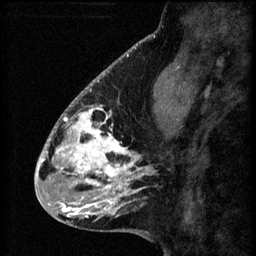
Breast MRI (dynamic contrast-enhanced), one sagittal slice. Position 20 of 60 along the scan axis. 3 images stored at this slice position (order not interpretable as contrast timing). 1.5 T. TE 4.2 ms, TR 8.2 ms. 2.2 mm slice thickness. 256 × 256 image matrix. Female patient, age 41 years.
Outlined on this slice (semi-automatically segmented with operator editing):
- analysis volume of interest (the breast-tissue region the enhancement analysis was run in; not a lesion): bounding box [x1, y1, x2, y2] px = [56, 104, 157, 207]
- tumour enhancement mask (voxels above the 70 % enhancement threshold inside the analysis volume of interest): [56, 106, 154, 207]